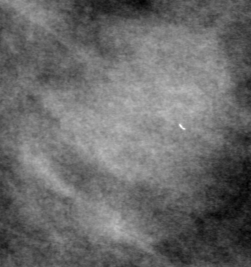
Cropped region of a digitized screen-film mammogram centred on a radiologist-marked abnormality; left breast; MLO view; BI-RADS breast density category 2 (scale 1–4).
- Finding: mass, shape oval, margins microlobulated; BI-RADS assessment category 0 (incomplete: needs additional imaging); subtlety rating 4 on a 1 (subtle) to 5 (obvious) scale; pathology (as recorded): benign.